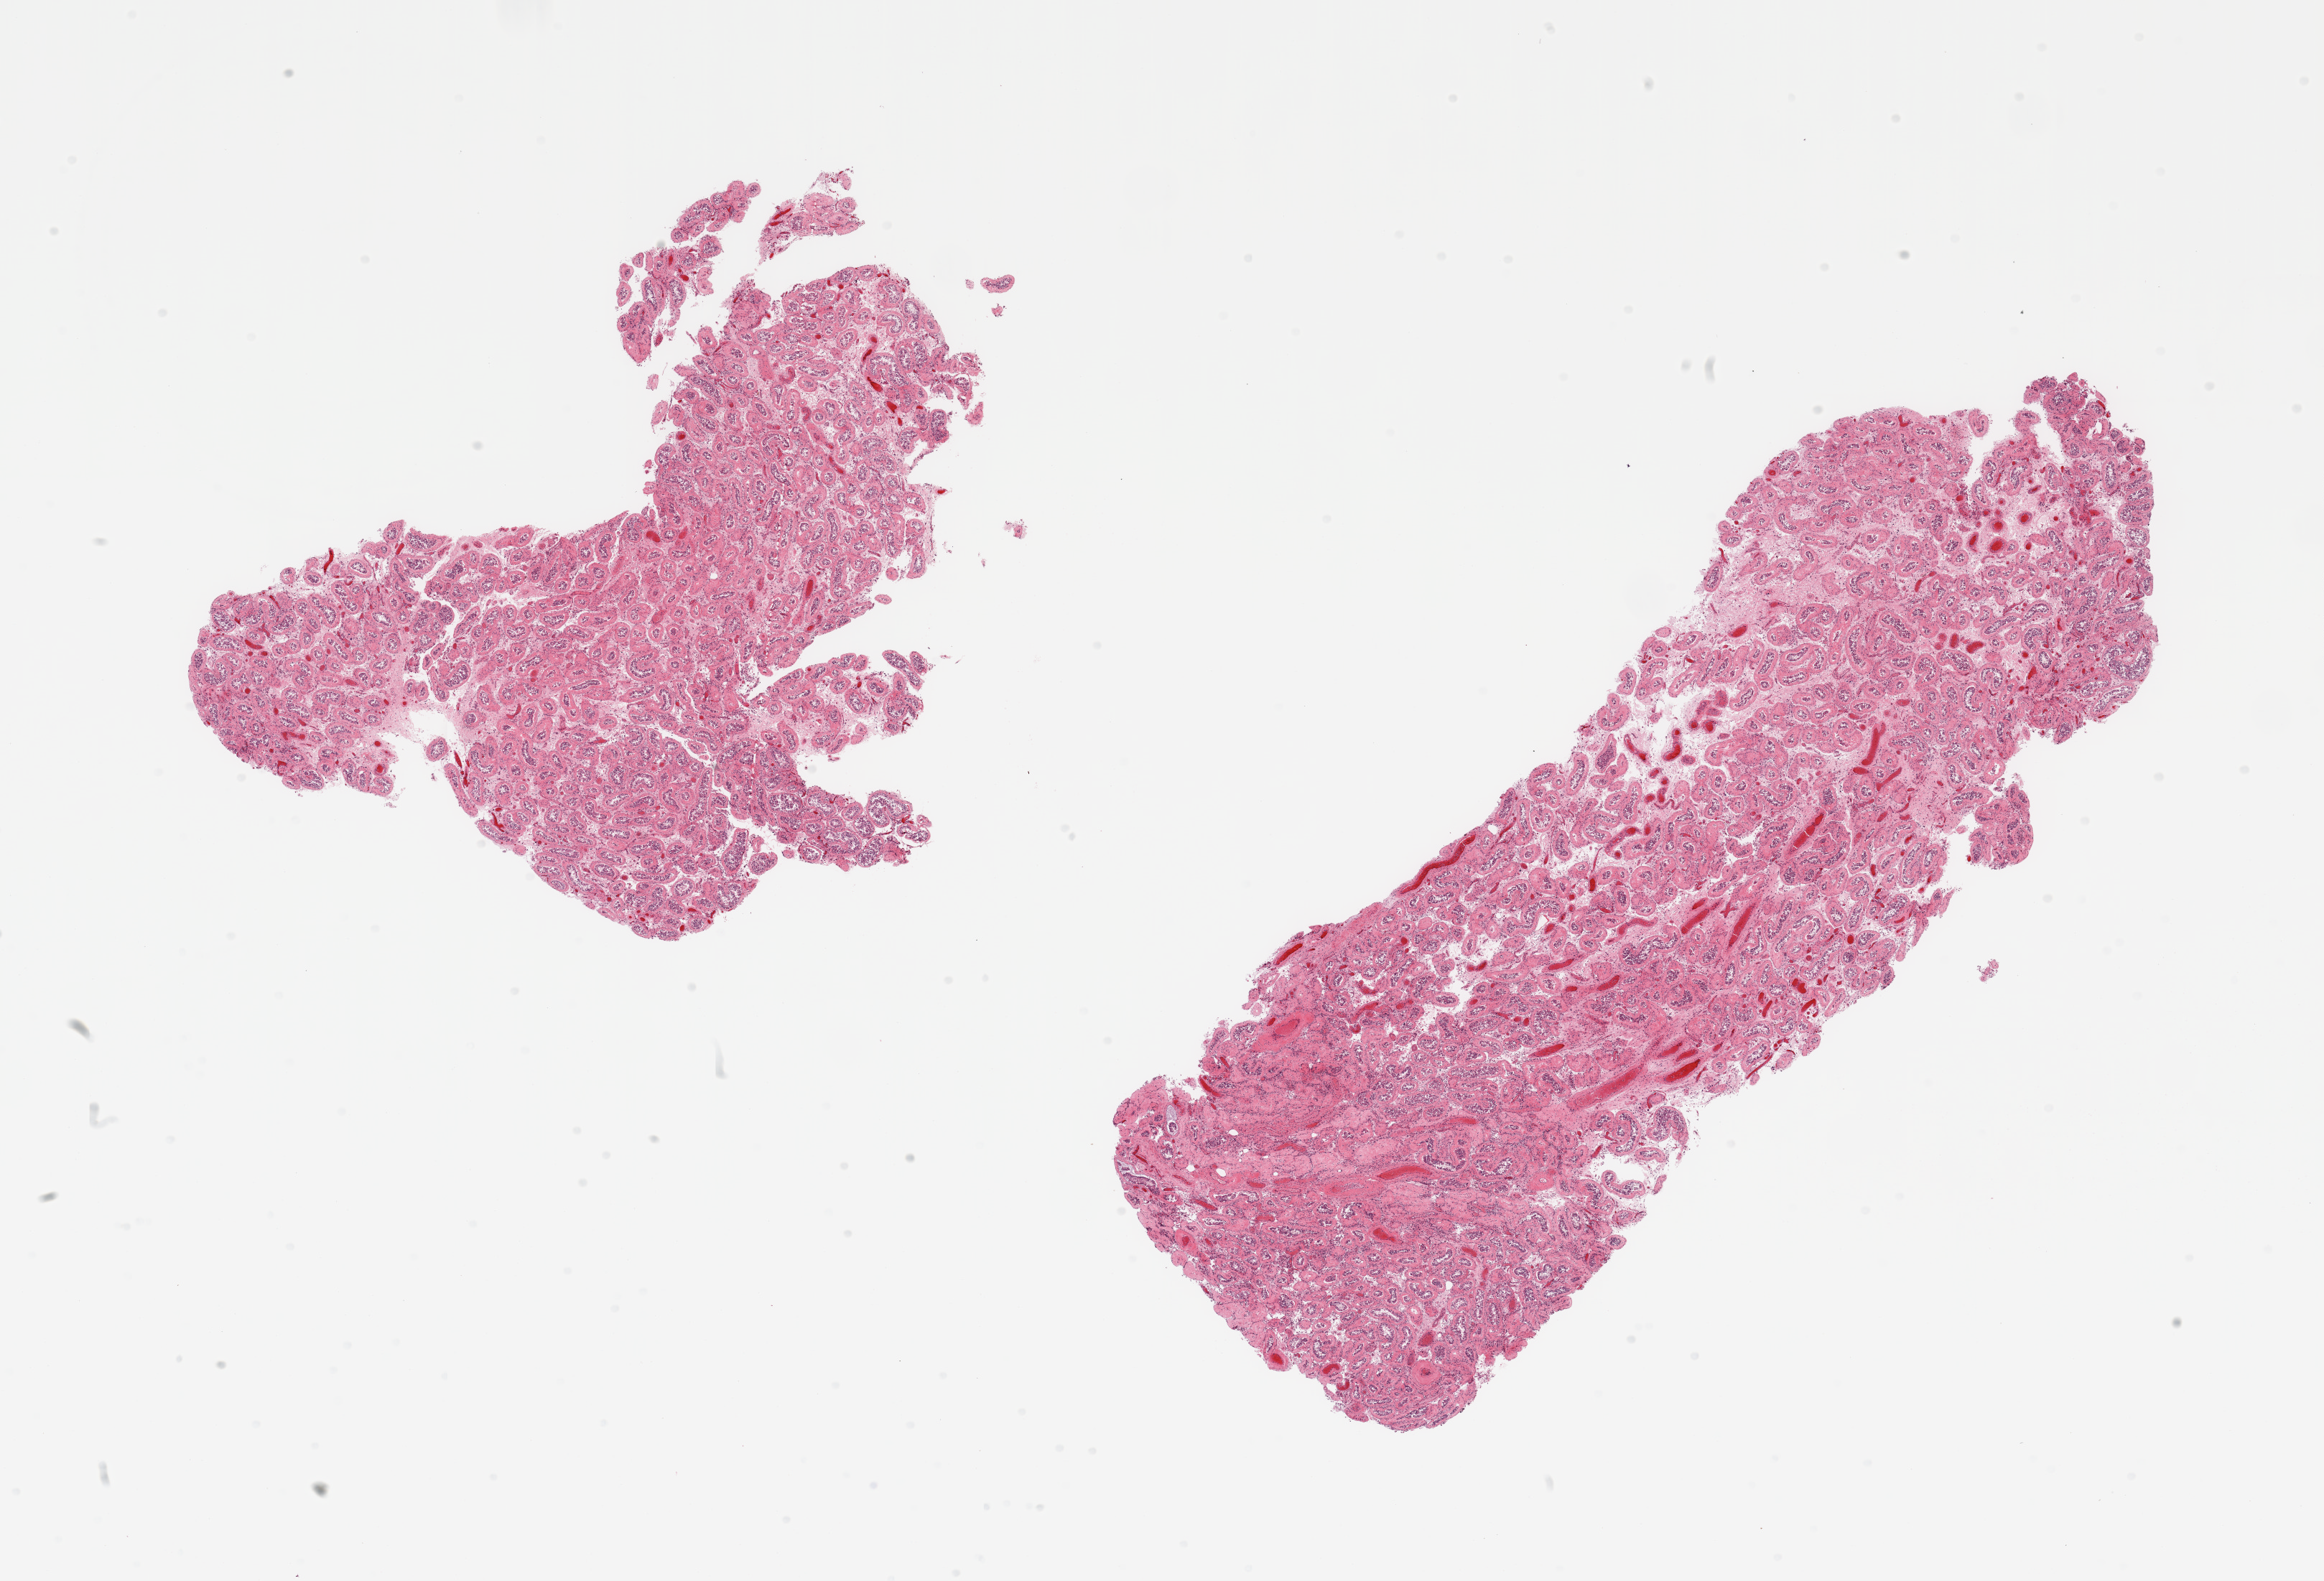
Digitized haematoxylin and eosin-stained section — whole scanned area (about 25.6 x 17.4 mm, acquisition: 20x scan) shown as a low-resolution overview; PAXgene-fixed, paraffin-embedded tissue; section of testis (target tissue); tissue donor sample.
Pathologist's review note for this sample: 2 pieces; diffuse marked thickening of tubular basement membrane and lack of mature spermatogenesis.